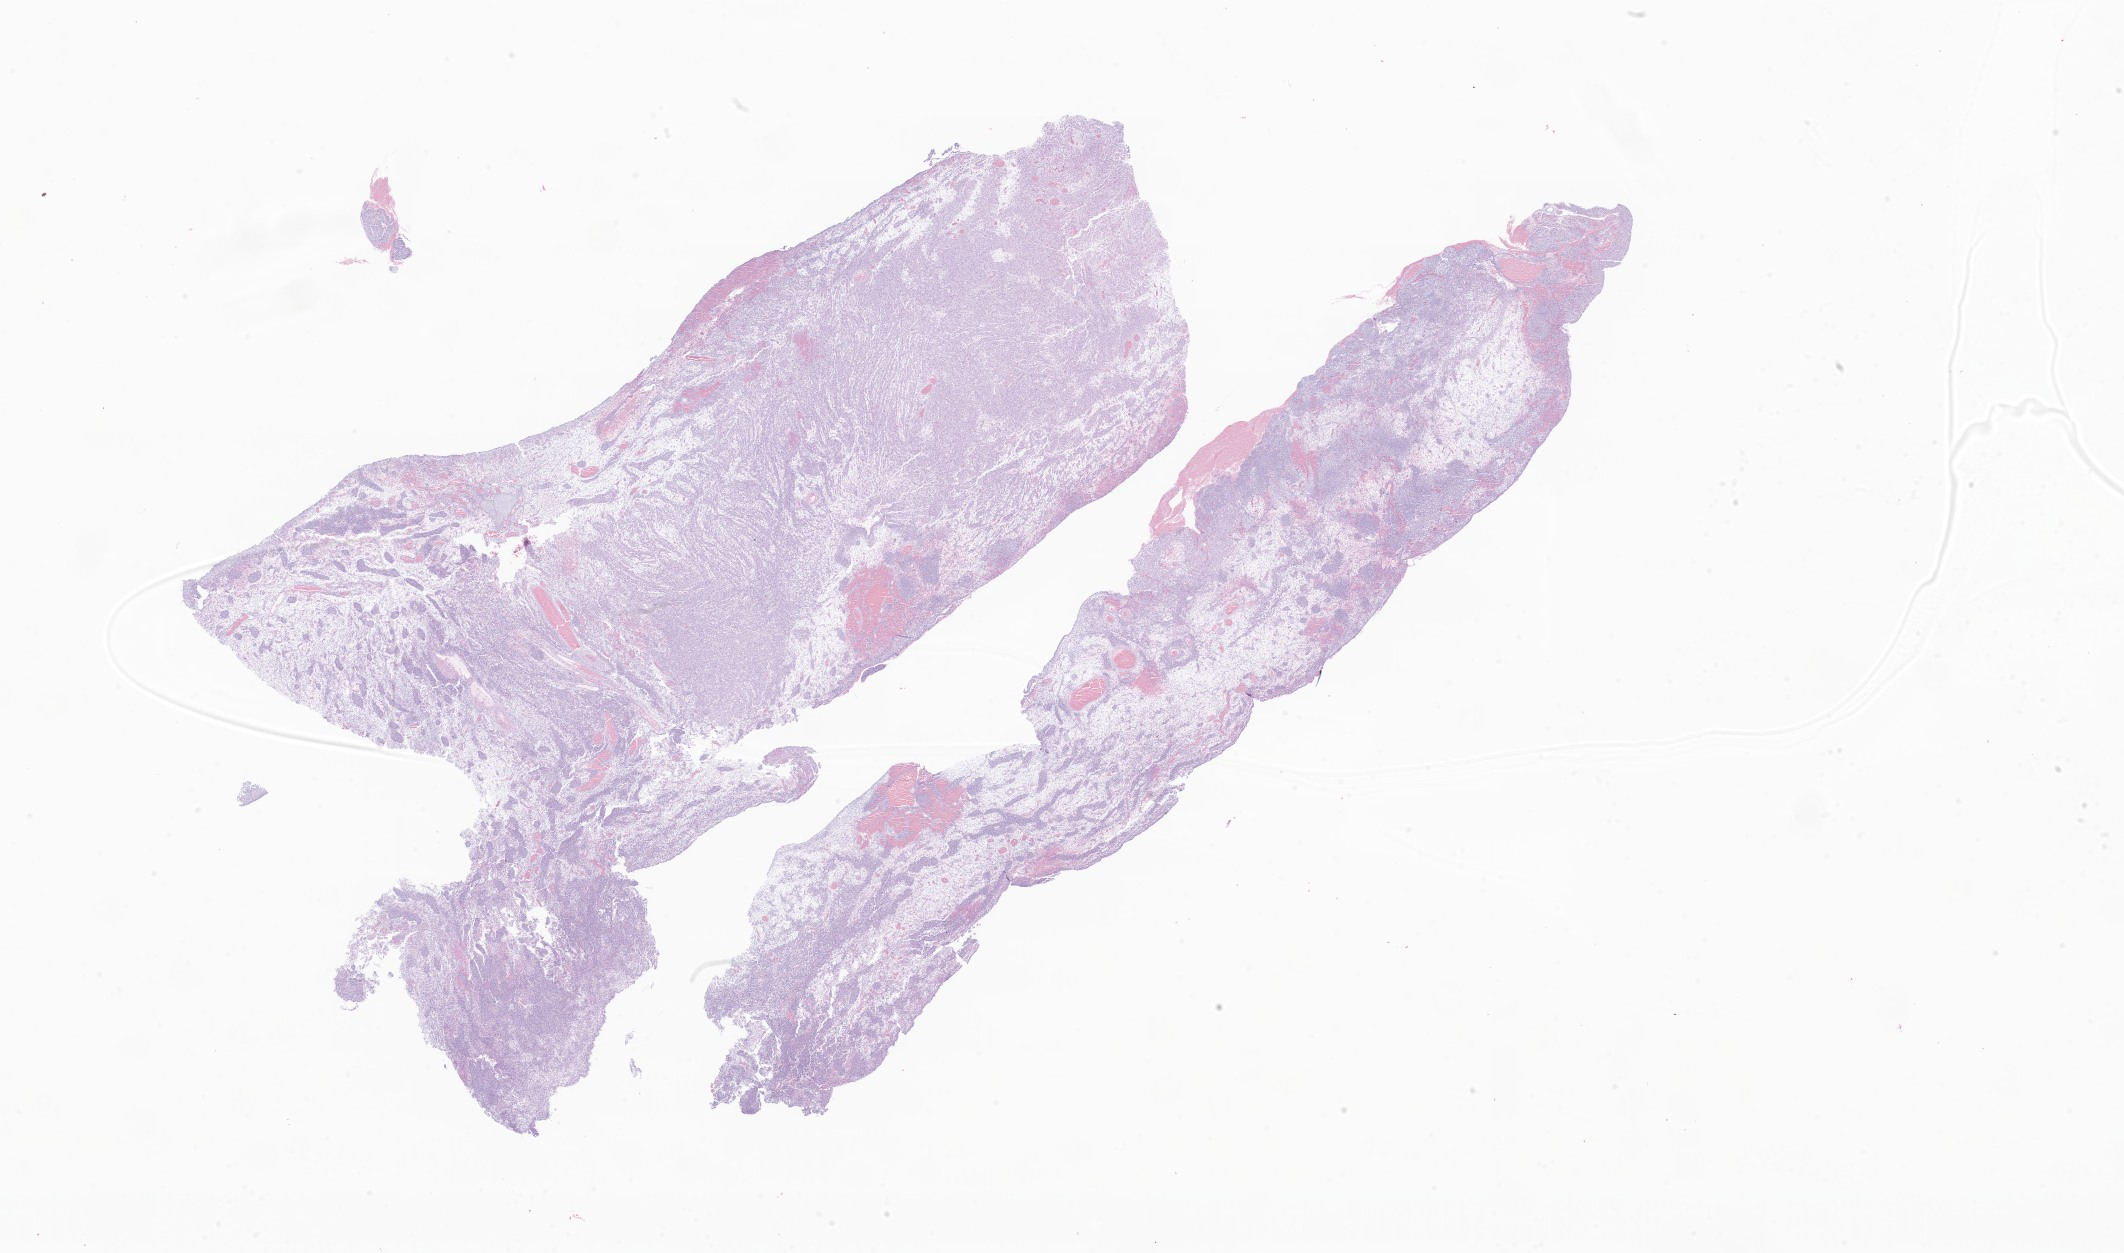
Digitized hematoxylin and eosin (H&E)-stained section of tumor tissue from the ovary, shown as a low-resolution overview of the whole scanned area (about 35.8 x 21.1 mm), FFPE section. Patient: female, age 217 months.
Recorded diagnosis: Sertoli-Leydig cell tumor, mod diff, with heterologous elements.